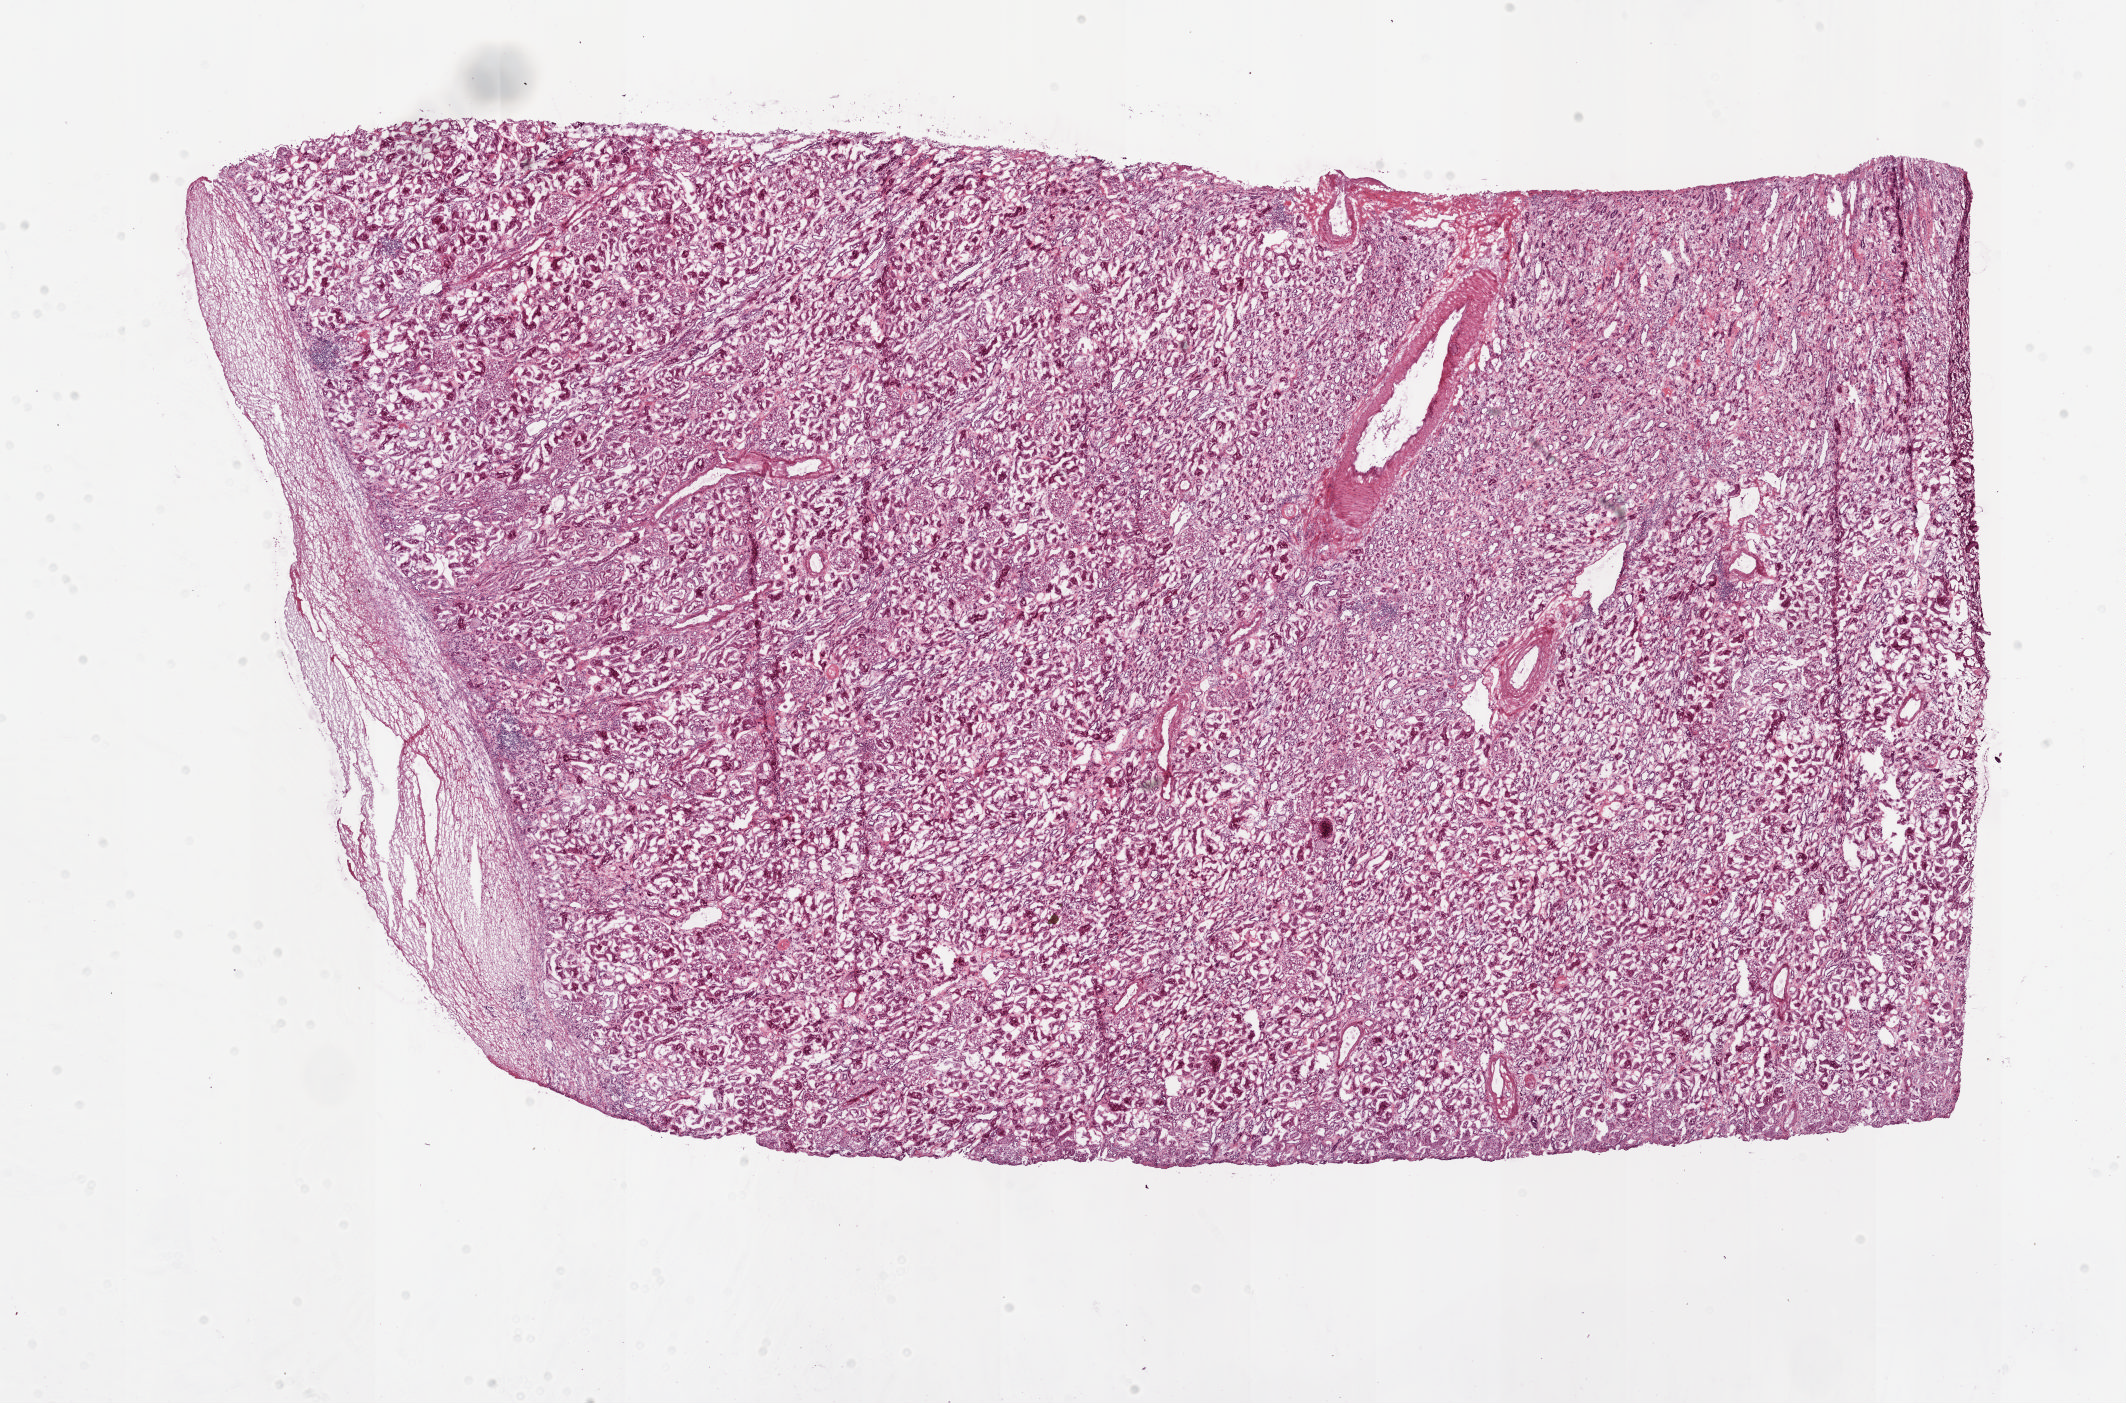
Digitized H&E-stained tissue section (whole slide) — a low-resolution overview of the entire scanned area, about 16.9 x 11.1 mm. Frozen section. Sample: solid tissue normal (non-tumour tissue), kidney. Female patient; age at initial diagnosis 72 years.
This section: solid tissue normal sample (biorepository sample class). Patient diagnosis: Clear cell adenocarcinoma, NOS.